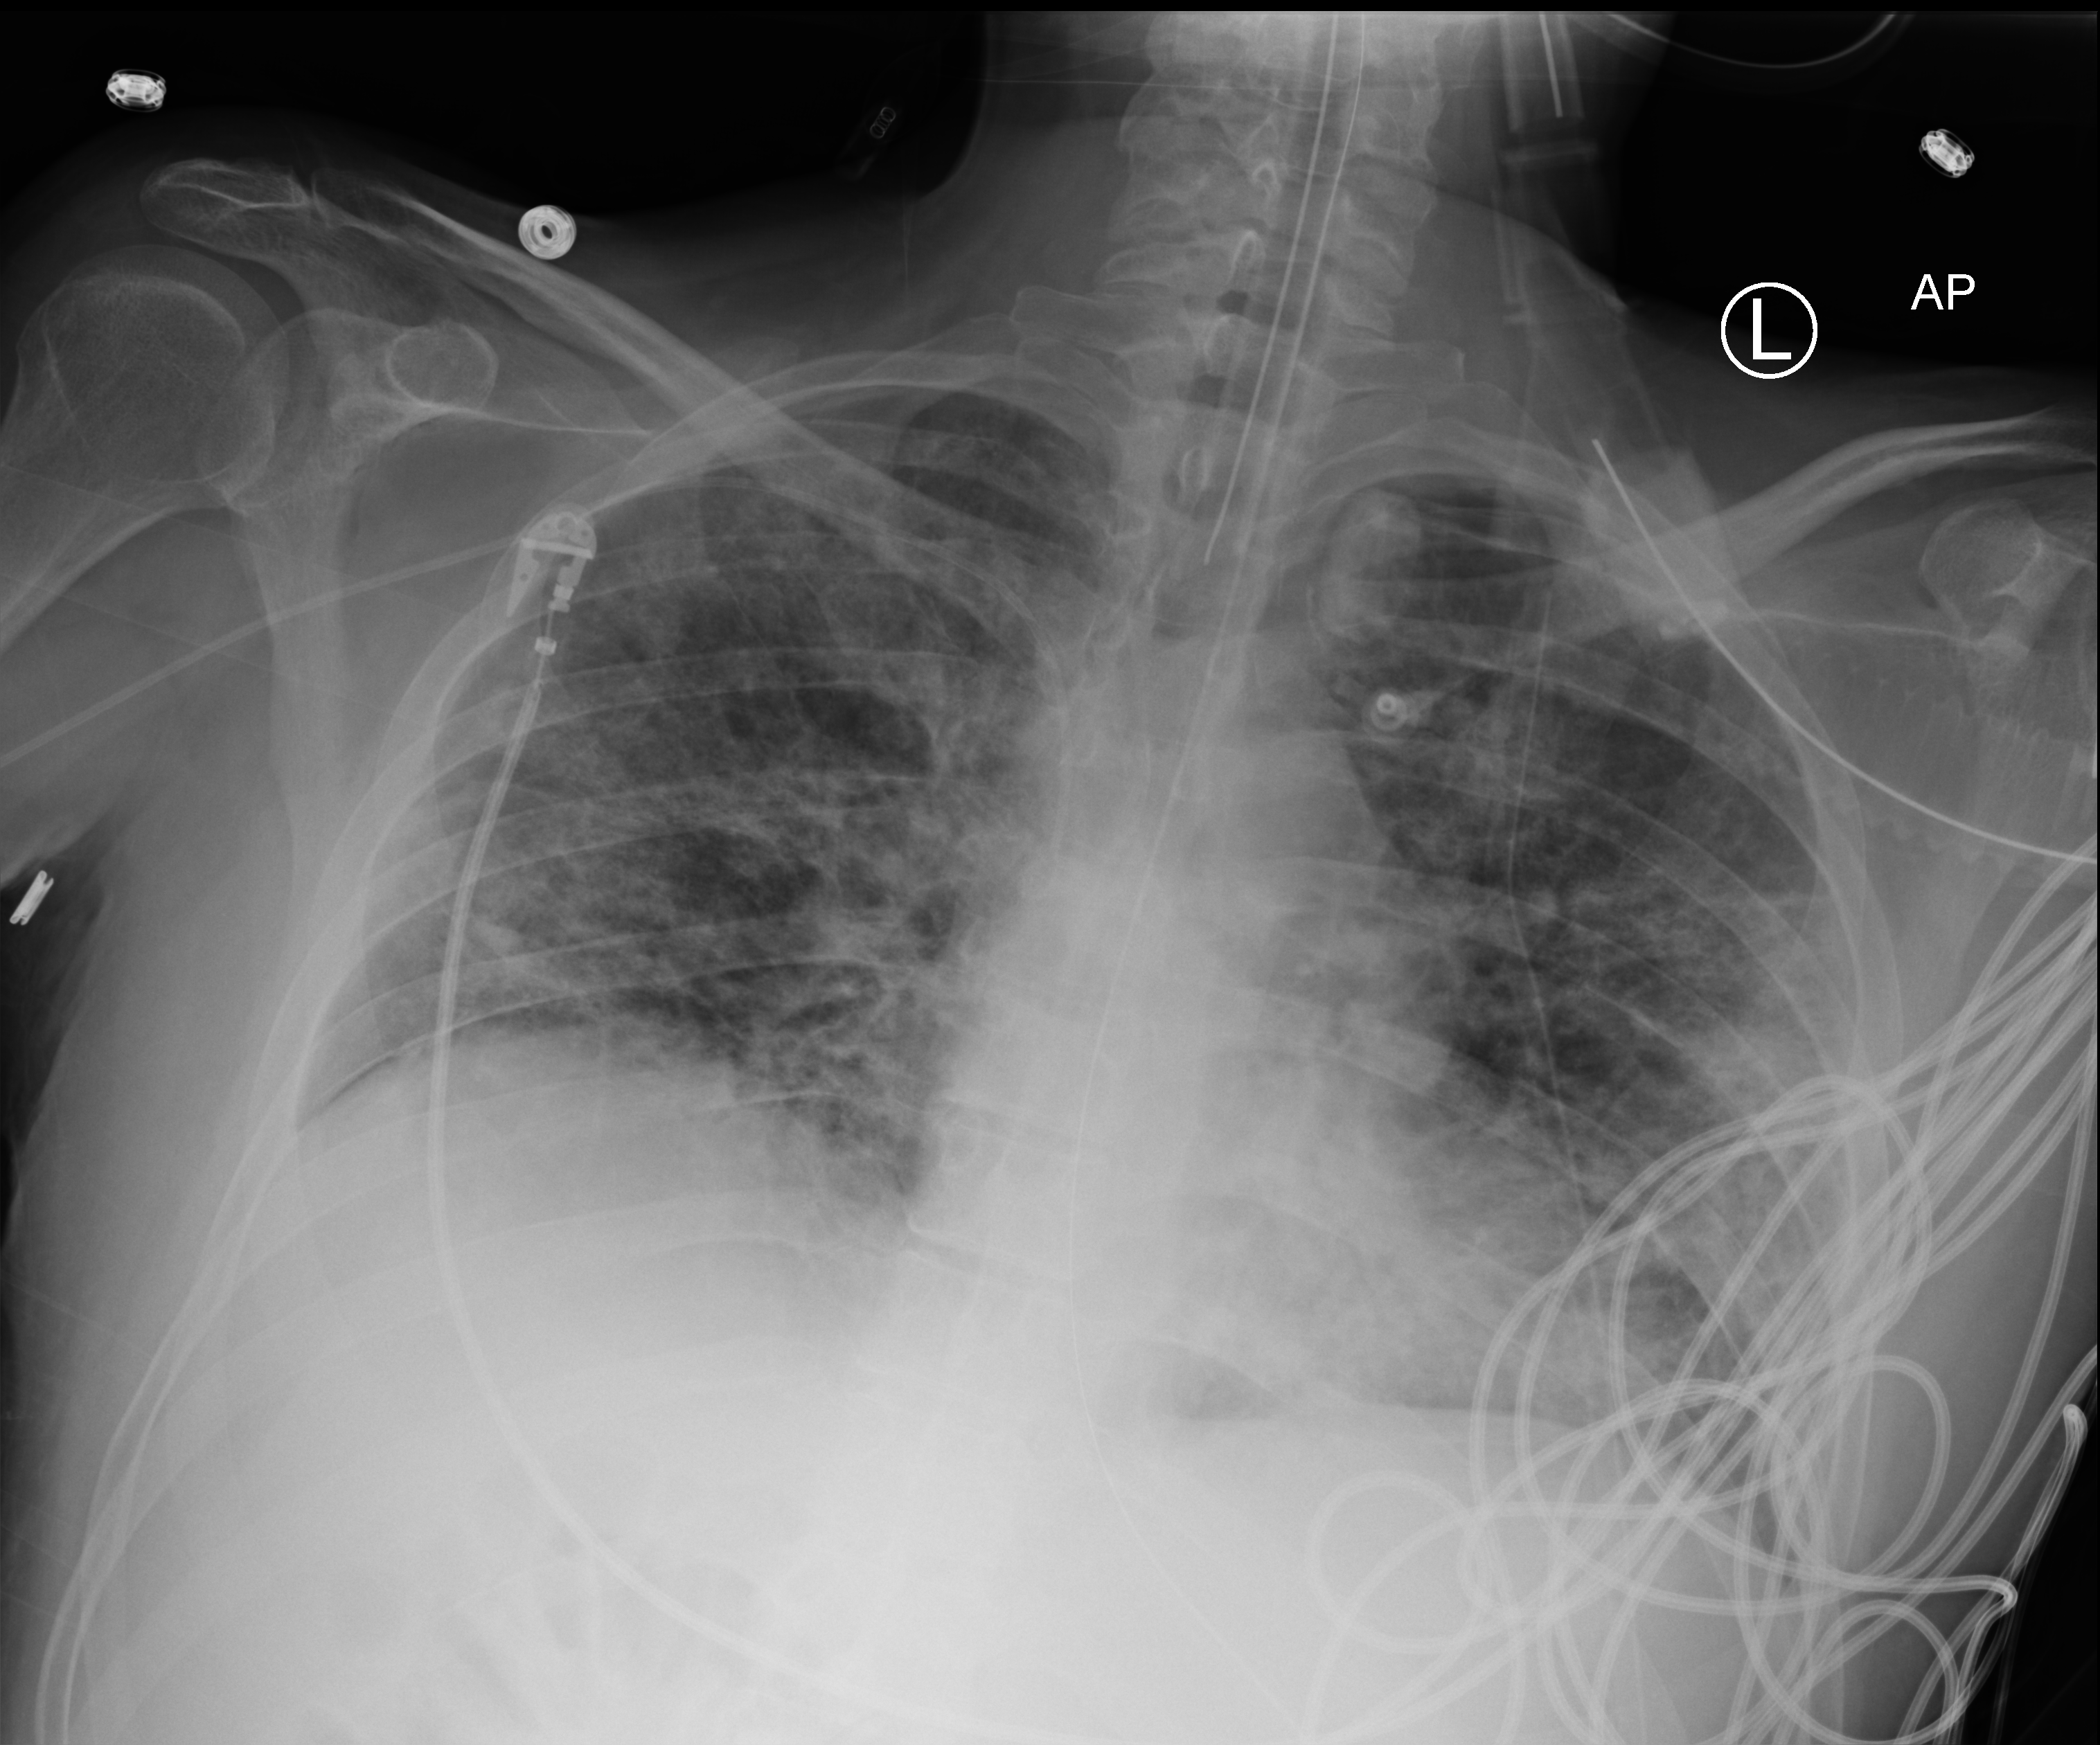
Portable chest radiograph. Patient hospitalised with COVID-19; male, aged 18–59 years.
Admission-level facts for this patient (not findings on this image; timing relative to this image not recorded):
- mechanically ventilated during this hospital stay: yes
- admitted to intensive care during this hospital stay: yes